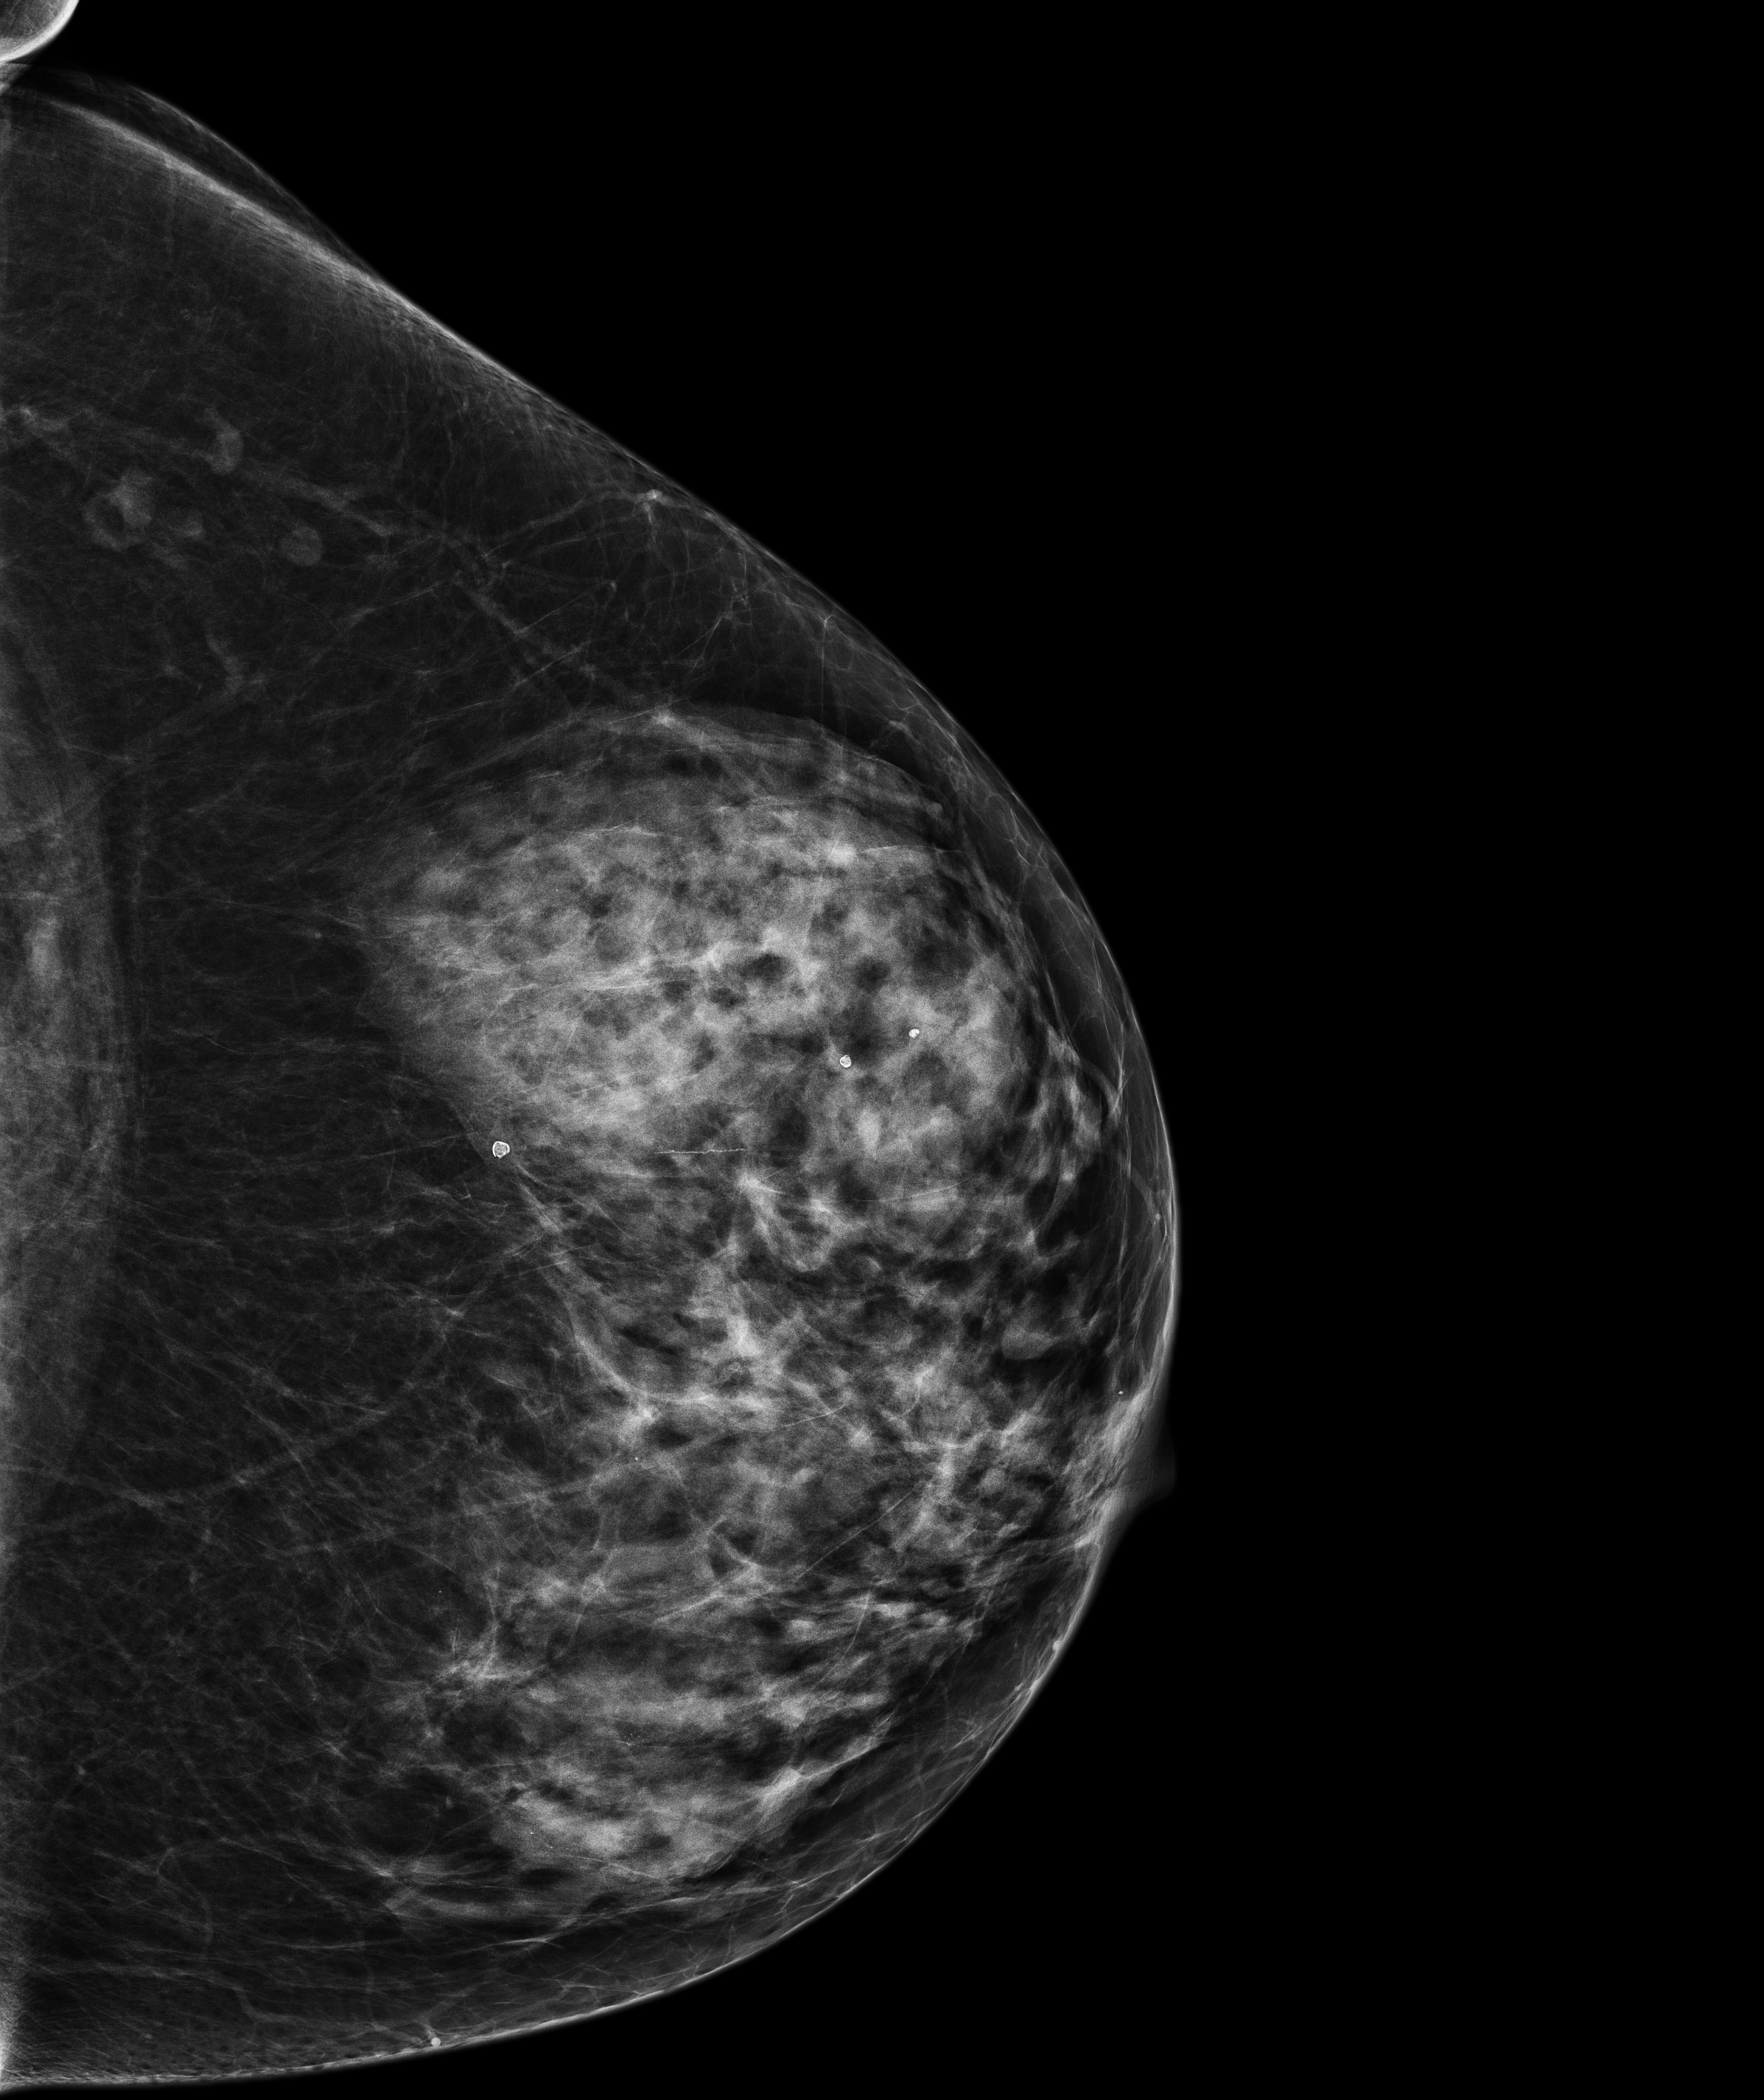
Screening examination, system: Senographe Pristina. Patient: female, 66 years.
Image type: full-field digital mammogram. Breast: left. Projection: CC view.